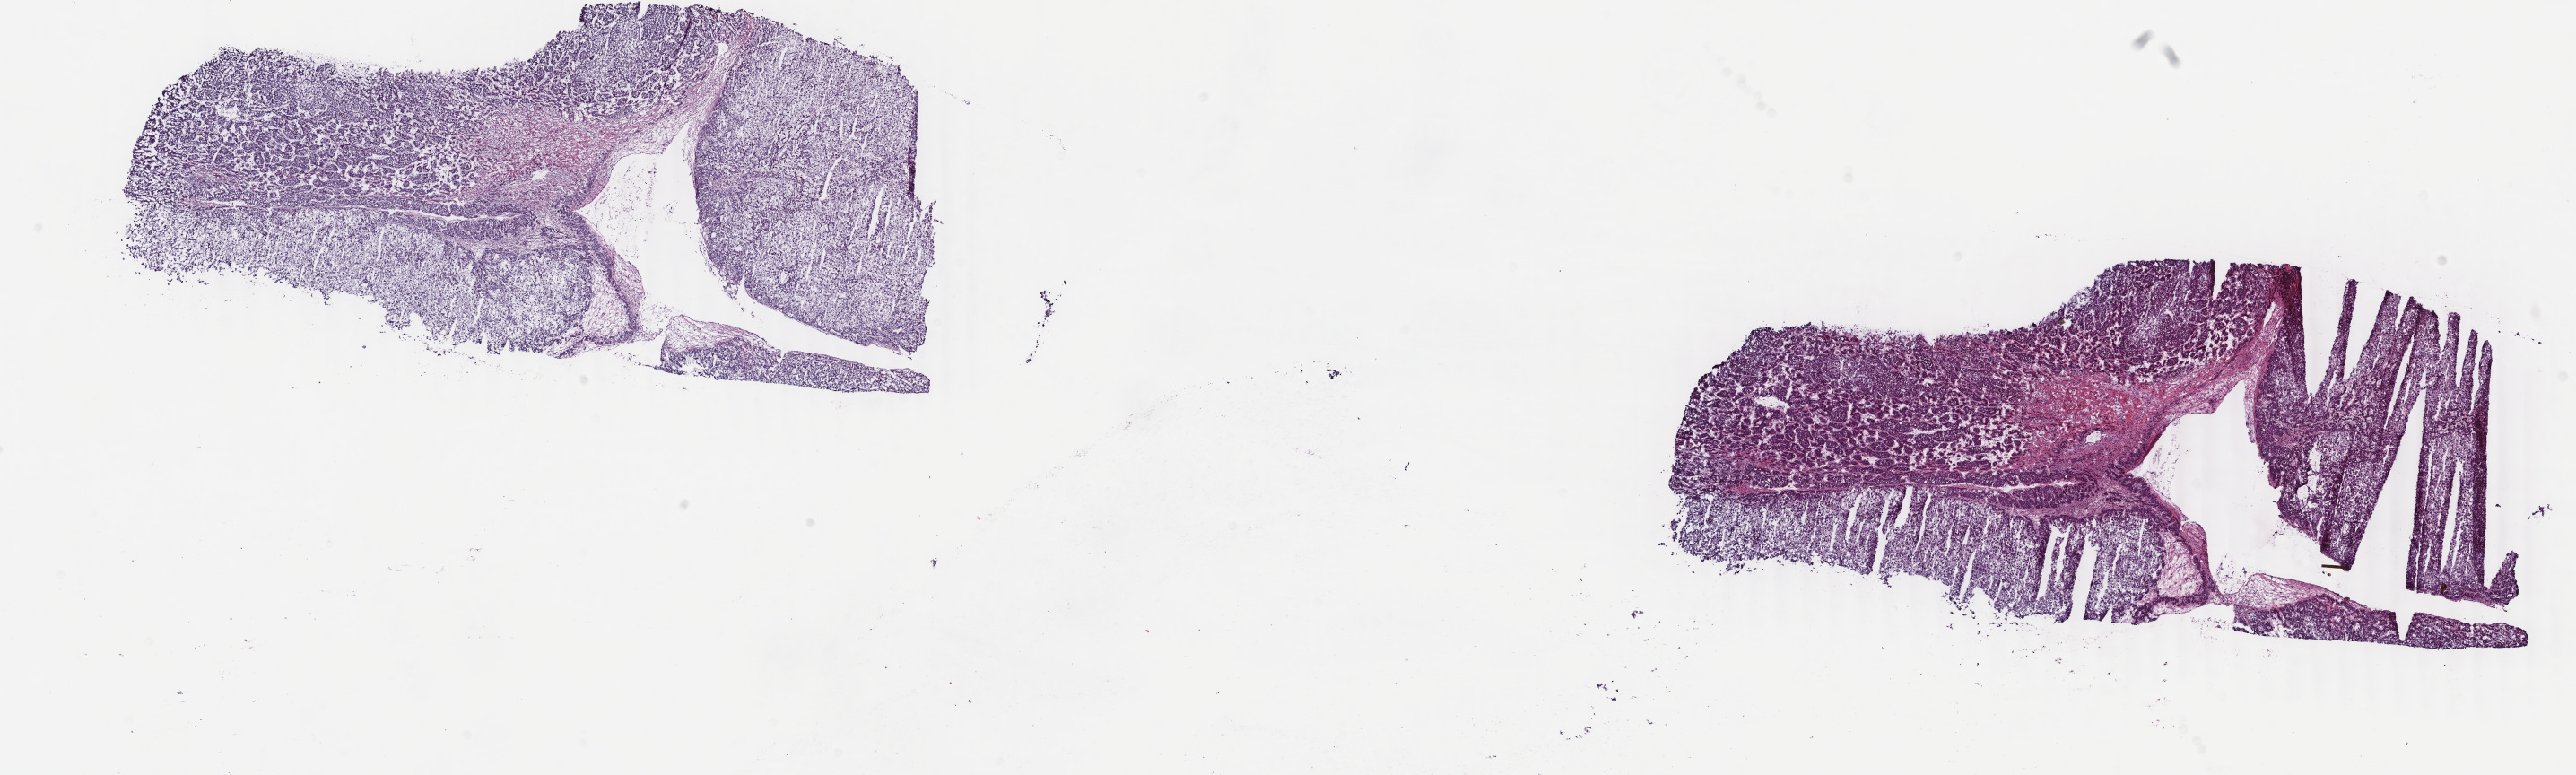
Hematoxylin and eosin (H&E) stained whole-slide image — low-resolution overview of the scanned area, about 22.8 x 6.9 mm, frozen section from the top of the tissue portion, primary tumour sample from the liver. Patient: female, age at initial diagnosis 57 years. Histologic grade: G2 (moderately differentiated). Pathologist review of this section (percent, as recorded): tumour cells 75%, tumour nuclei 80%, normal cells 0%, stromal cells 20%, necrosis 5%. Infiltration values recorded for this section: lymphocyte infiltration 3%, monocyte infiltration 2%, neutrophil infiltration 0%.
TNM: T1 N0 M0. AJCC pathologic stage: I (6th edition). Diagnosis: Hepatocellular carcinoma, NOS.